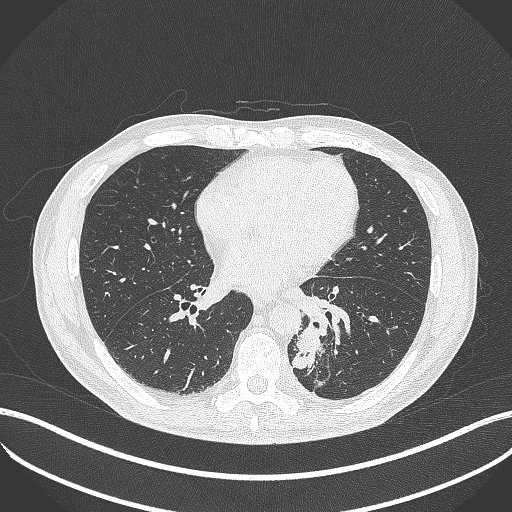
Chest CT, one axial slice; slice 169 of 451 in the series (ordered by position); reconstruction kernel B70f; lung window (W 1500 / L -600 HU); 1 mm slice thickness; 512 × 512 image matrix. Male patient, age 72 years. Case-level facts recorded for this patient, not image findings: clinical TNM (as recorded): T2b N0 M1.
Outlined on this slice (bounding box drawn by a radiologist):
- lung tumour (recorded histology: adenocarcinoma): bounding box <290,318,329,371> (left, top, right, bottom; pixels)